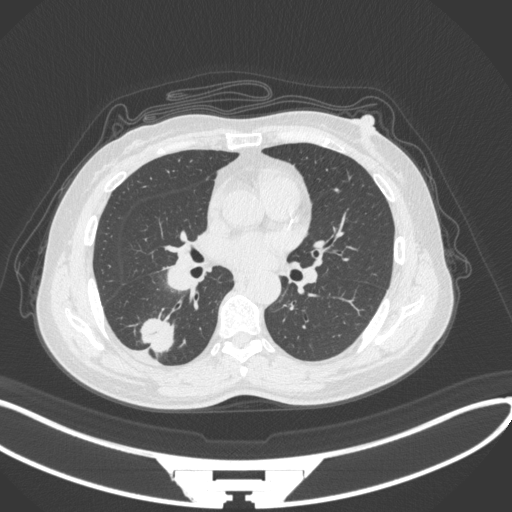
Chest CT, one axial slice. Slice 152 of 352 in the series (ordered by position). Lung window (W 1500 / L -600 HU). 512 × 512 image matrix, field of view 400 × 400 mm. Female patient, age 55 years. Case-level facts recorded for this patient, not image findings: clinical TNM (as recorded): T1c N1 M0.
Outlined on this slice (rectangle marked by the reading radiologist):
- lung tumour (recorded histology: adenocarcinoma): bounding box (x1, y1, x2, y2) in pixels: (136, 315, 180, 360)